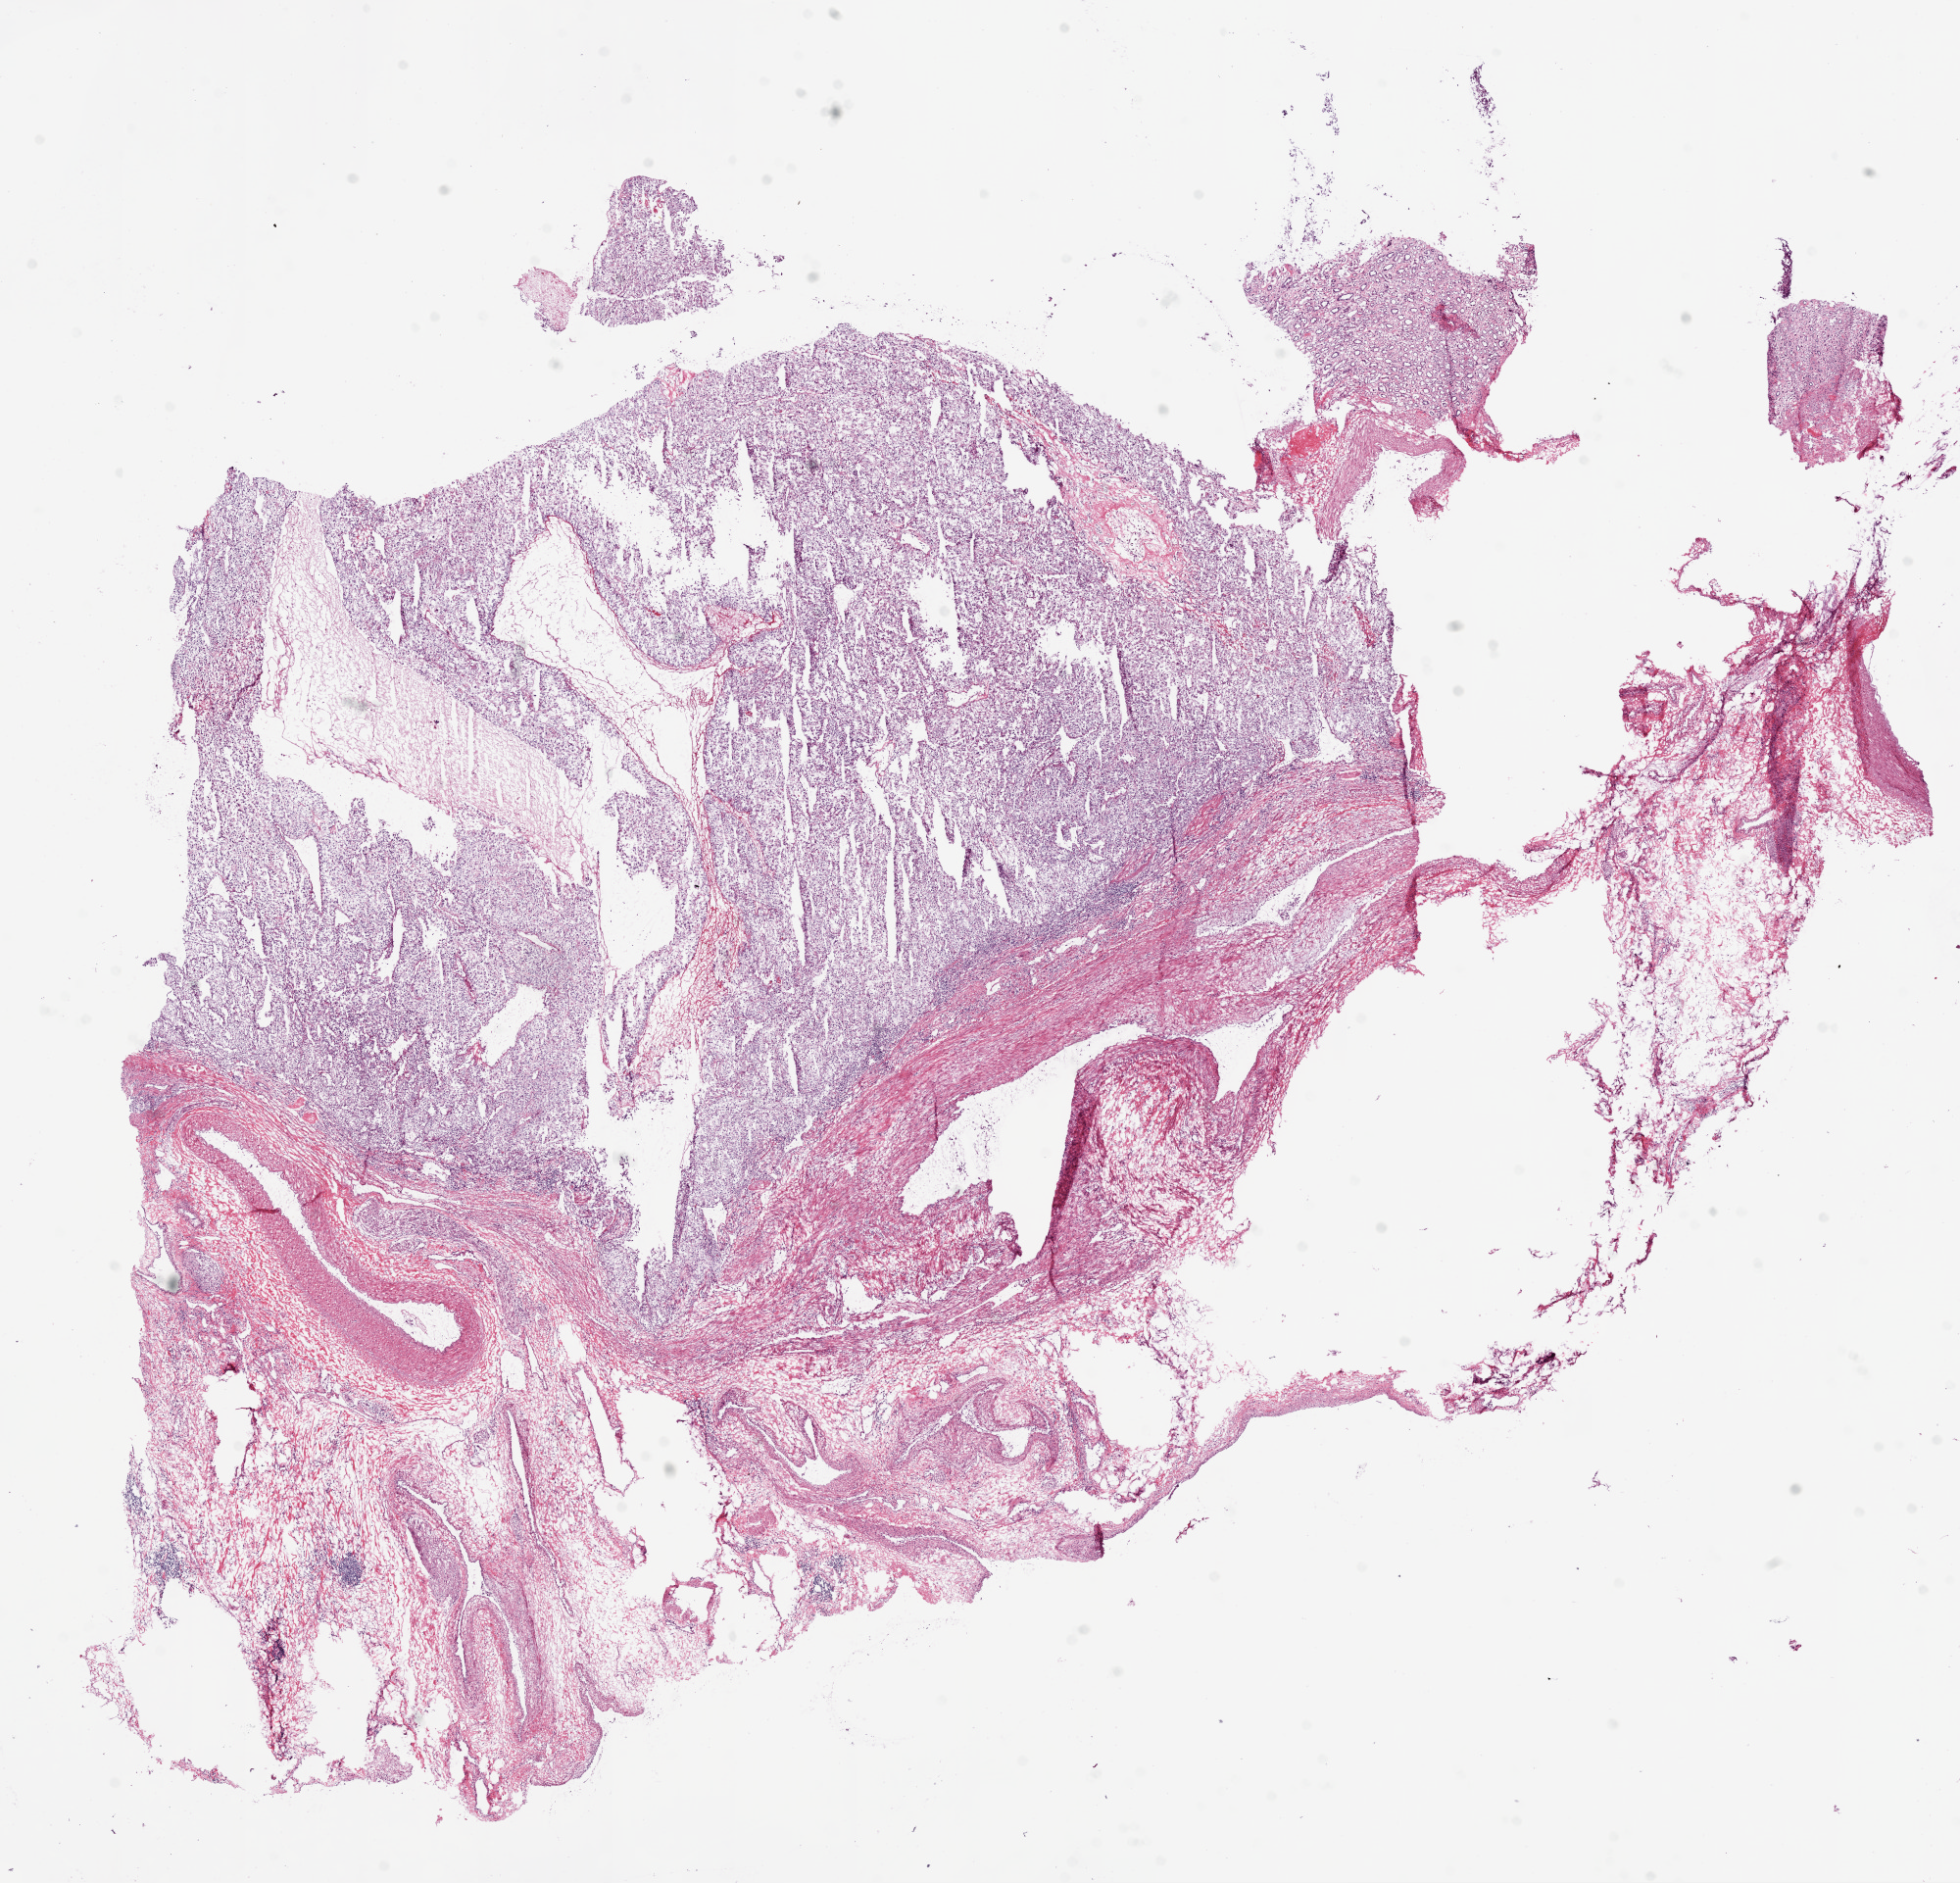
H&E-stained whole-slide image — whole scanned area (about 16.0 x 15.4 mm) shown as a low-resolution overview; frozen section from the bottom of the tissue portion; primary tumour sample from the kidney. Male, age 61 years at initial diagnosis. Histologic grade: G3 (poorly differentiated). Composition of this section per pathologist review: tumour cells 70%, tumour nuclei 75%, normal cells 0%, stromal cells 30%, necrosis 0%.
* diagnosis: Clear cell adenocarcinoma, NOS
* AJCC pathologic stage: IV
* laterality: right